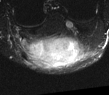
MRI of an extremity soft-tissue mass, one axial slice. Position 15 of 52 along the scan axis. T2-weighted fat-saturated. MR volume resampled by the dataset authors to the PET/CT grid (not the native acquisition matrix). 3.27 mm slice thickness. 109 × 95 image matrix, field of view 106 × 93 mm. Male patient. From the clinical record (not read from this slice): histological type: synovial sarcoma; site of the primary tumour: left poplietal fossa.
Annotated regions visible in this slice (expert contour drawn on MRI and transferred to this co-registered scan by the dataset authors):
- gross tumour volume (mass): box from (x=26, y=33) to (x=82, y=68) px